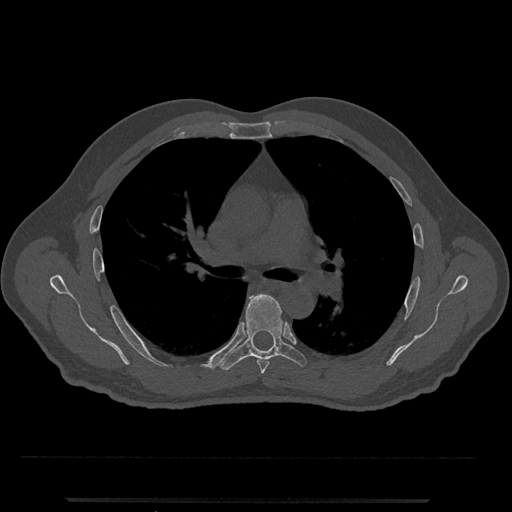
CT including the spine, one axial slice; slice 754 of 797 in the series (ordered by position); reconstruction kernel Br40s/3; bone window (W 1800 / L 400 HU); 0.5 mm slice thickness; 512 × 512 image matrix, field of view 419 × 419 mm. Male patient, age 63 years. Case-level facts recorded for this patient, not image findings: primary cancer: prostate.
Outlined on this slice (semi-automatic segmentation, software-assisted and operator-edited):
- T5 vertebra: bounding box [x1, y1, x2, y2] px = [257, 359, 270, 374]
- T6 vertebra: [219, 293, 307, 371]